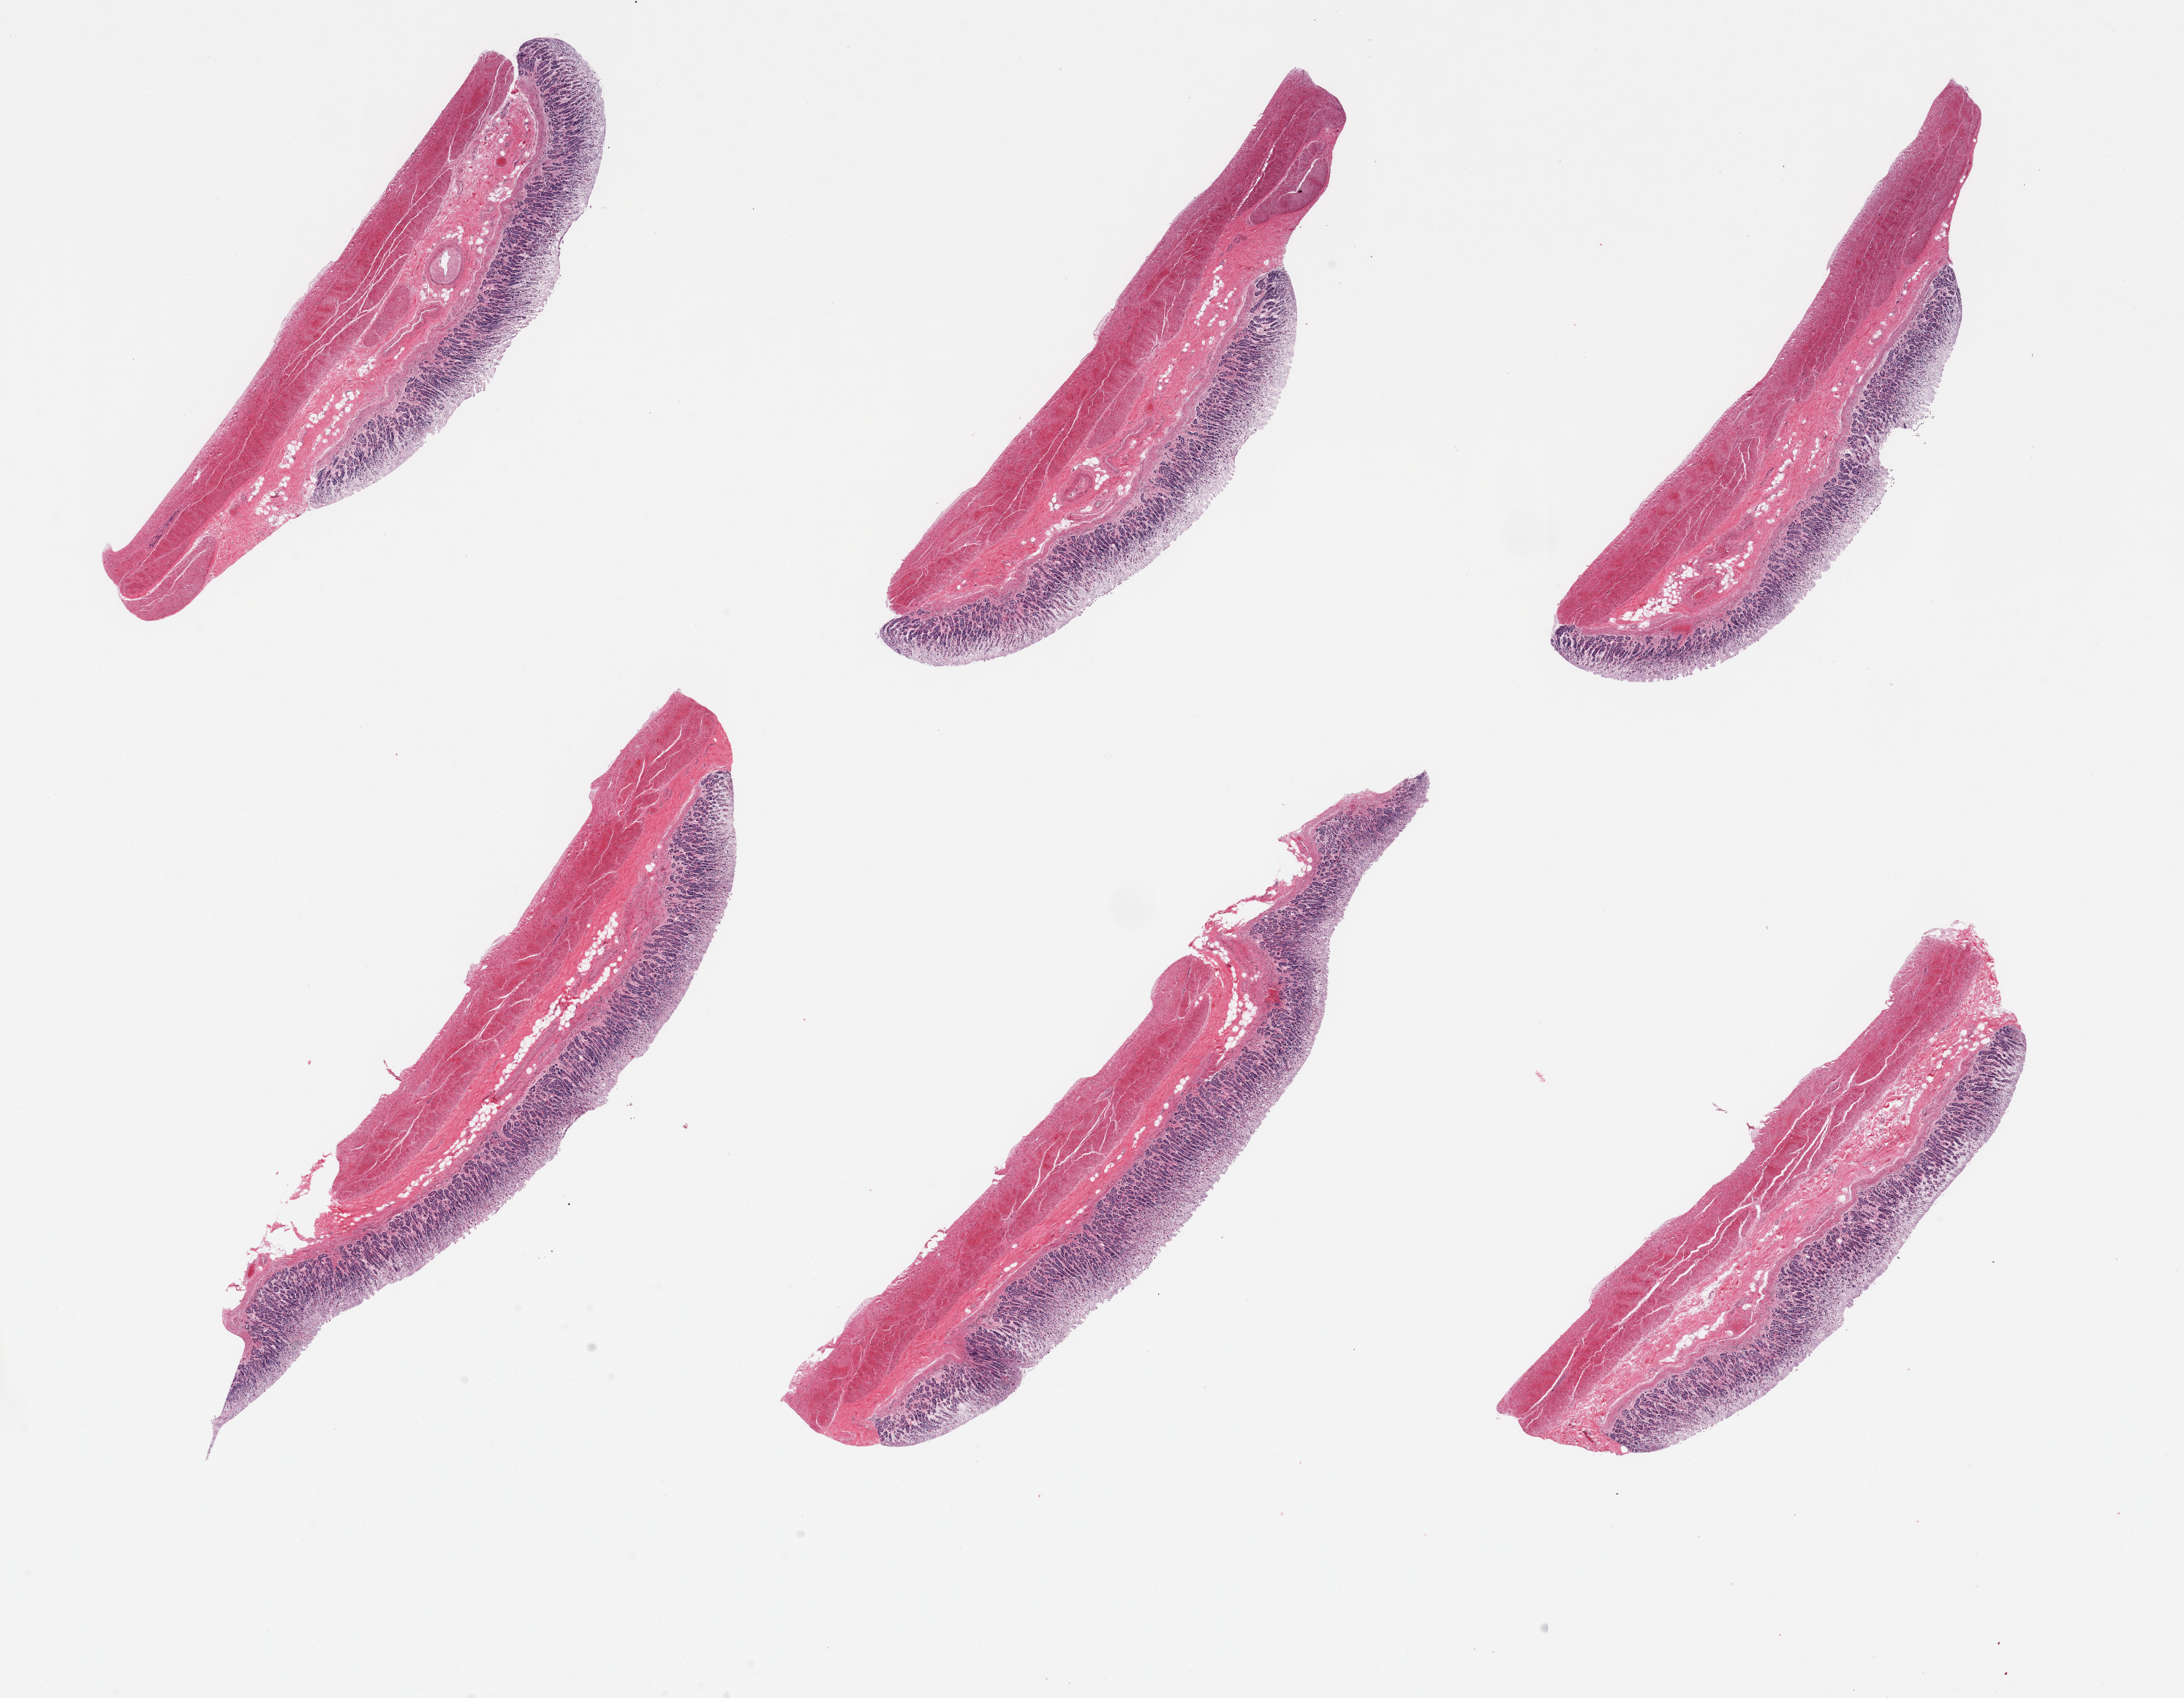
Whole-slide image, H&E stain, brightfield — whole scanned area (about 23.6 x 18.4 mm, from a 20x scan) shown as a low-resolution overview. PAXgene-fixed paraffin-embedded (PFPE) section. Section of stomach (target tissue). Tissue donor sample. Donor: male.
- review note (as recorded): 6 pieces; superficial glands severely autolyzed